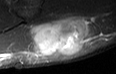
MRI of an extremity soft-tissue mass, one axial slice; slice 17 of 36 in the series (ordered by position); STIR; MR volume resampled by the dataset authors to the PET/CT grid (not the native acquisition matrix); 3.27 mm slice thickness; 116 × 74 image matrix. Male patient. From the clinical record (not read from this slice): histological type: pleiomorphic leiomyosarcoma; grade: high; site of the primary tumour: left buttock.
Annotated regions visible in this slice (expert contour drawn on MRI and transferred to this co-registered scan by the dataset authors):
- gross tumour volume including surrounding oedema: bounding box [x1, y1, x2, y2] px = [27, 17, 85, 56]
- gross tumour volume (mass): [27, 17, 85, 56]